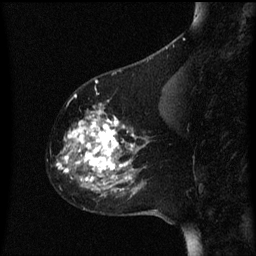
Breast MRI (dynamic contrast-enhanced), one sagittal slice; slice 21 of 60 in the series (ordered by position); dynamic contrast-enhanced series, image 2 of 3 at this slice position (ordered by acquisition); 1.5 T; TE 4.2 ms, TR 8 ms; 2 mm slice thickness; 256 × 256 image matrix, field of view 200 × 200 mm. Female patient, age 60 years.
Outlined on this slice (semi-automatic segmentation, software-assisted and operator-edited):
- analysis volume of interest (the breast-tissue region the enhancement analysis was run in; not a lesion): bounding box (x1, y1, x2, y2) in pixels: (55, 102, 151, 197)
- tumour enhancement mask (voxels above the 70 % enhancement threshold inside the analysis volume of interest): (57, 108, 137, 191)